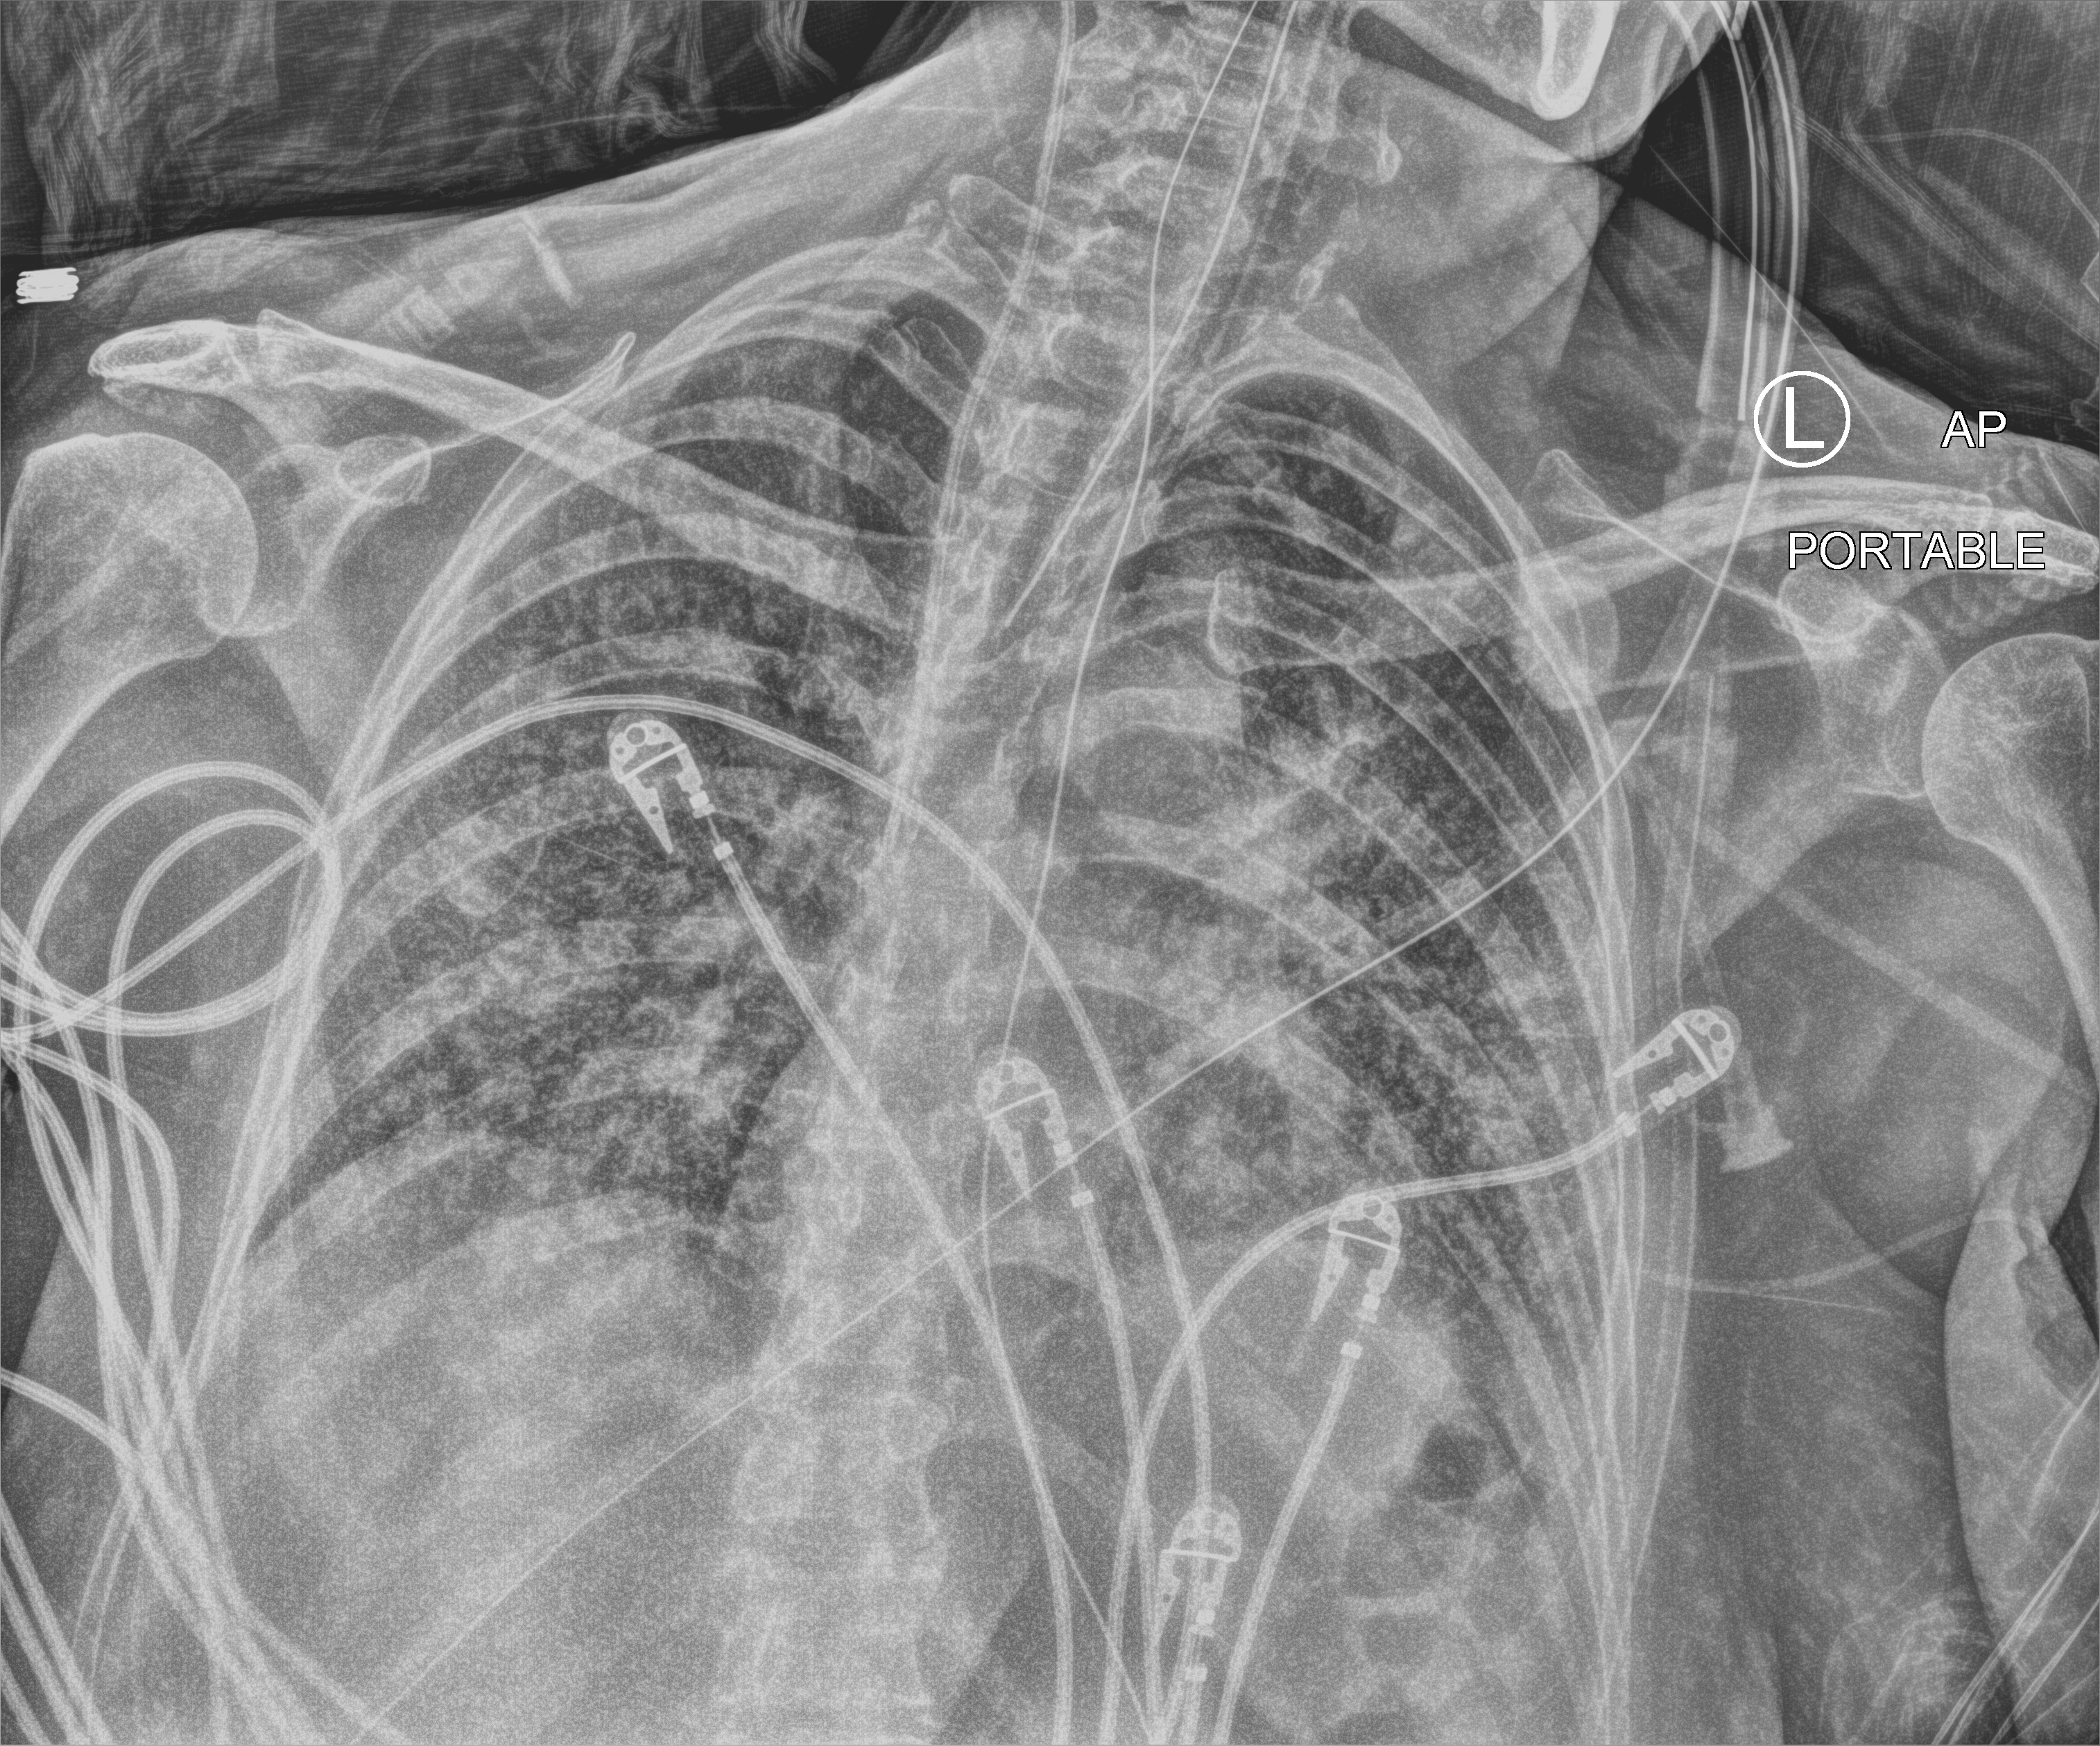
Bedside chest radiograph (computed radiography); anteroposterior (AP) projection. Female patient hospitalised with COVID-19, age 60–74 years.
Admission-level facts for this patient (not findings on this image; timing relative to this image not recorded):
- other chronic lung disease (admission record): no